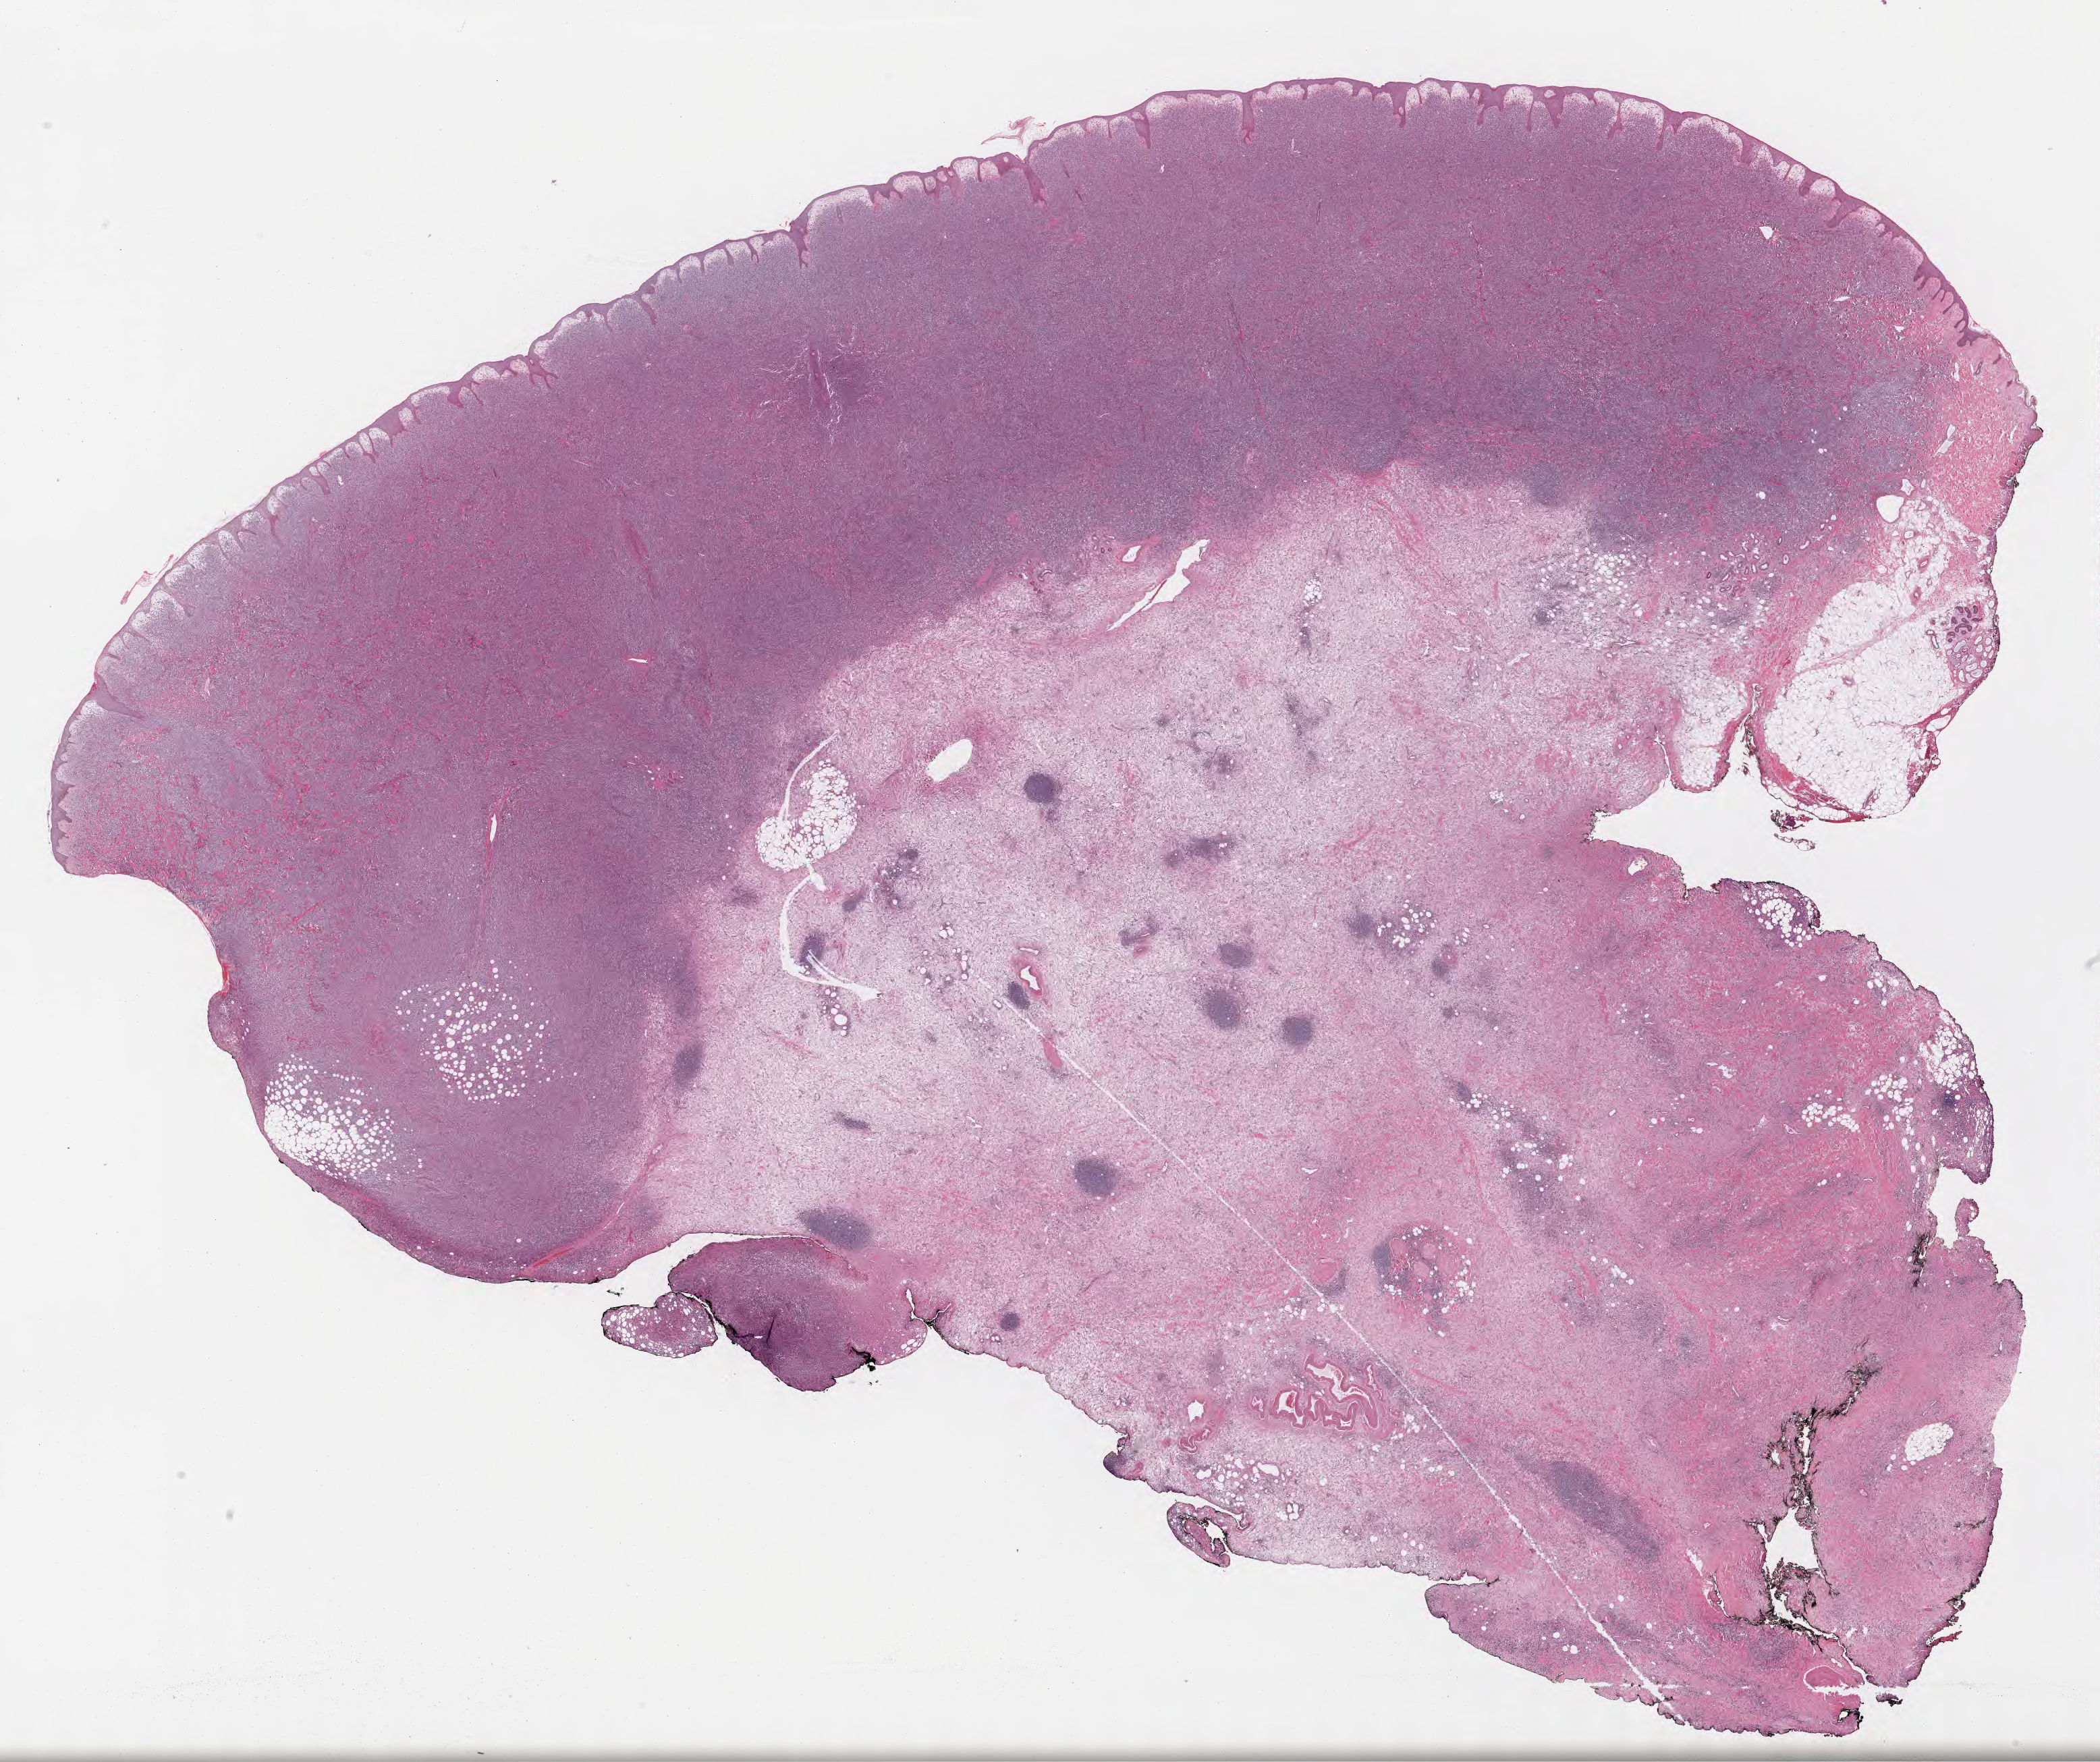
Whole-slide image, H&E stain — whole scanned area (about 25.1 x 21.1 mm) shown as a low-resolution overview; tumor tissue; anatomic site: lymph node. Patient: male, age 52 years.
Histologic diagnosis: Diffuse large B-cell lymphoma, NOS.